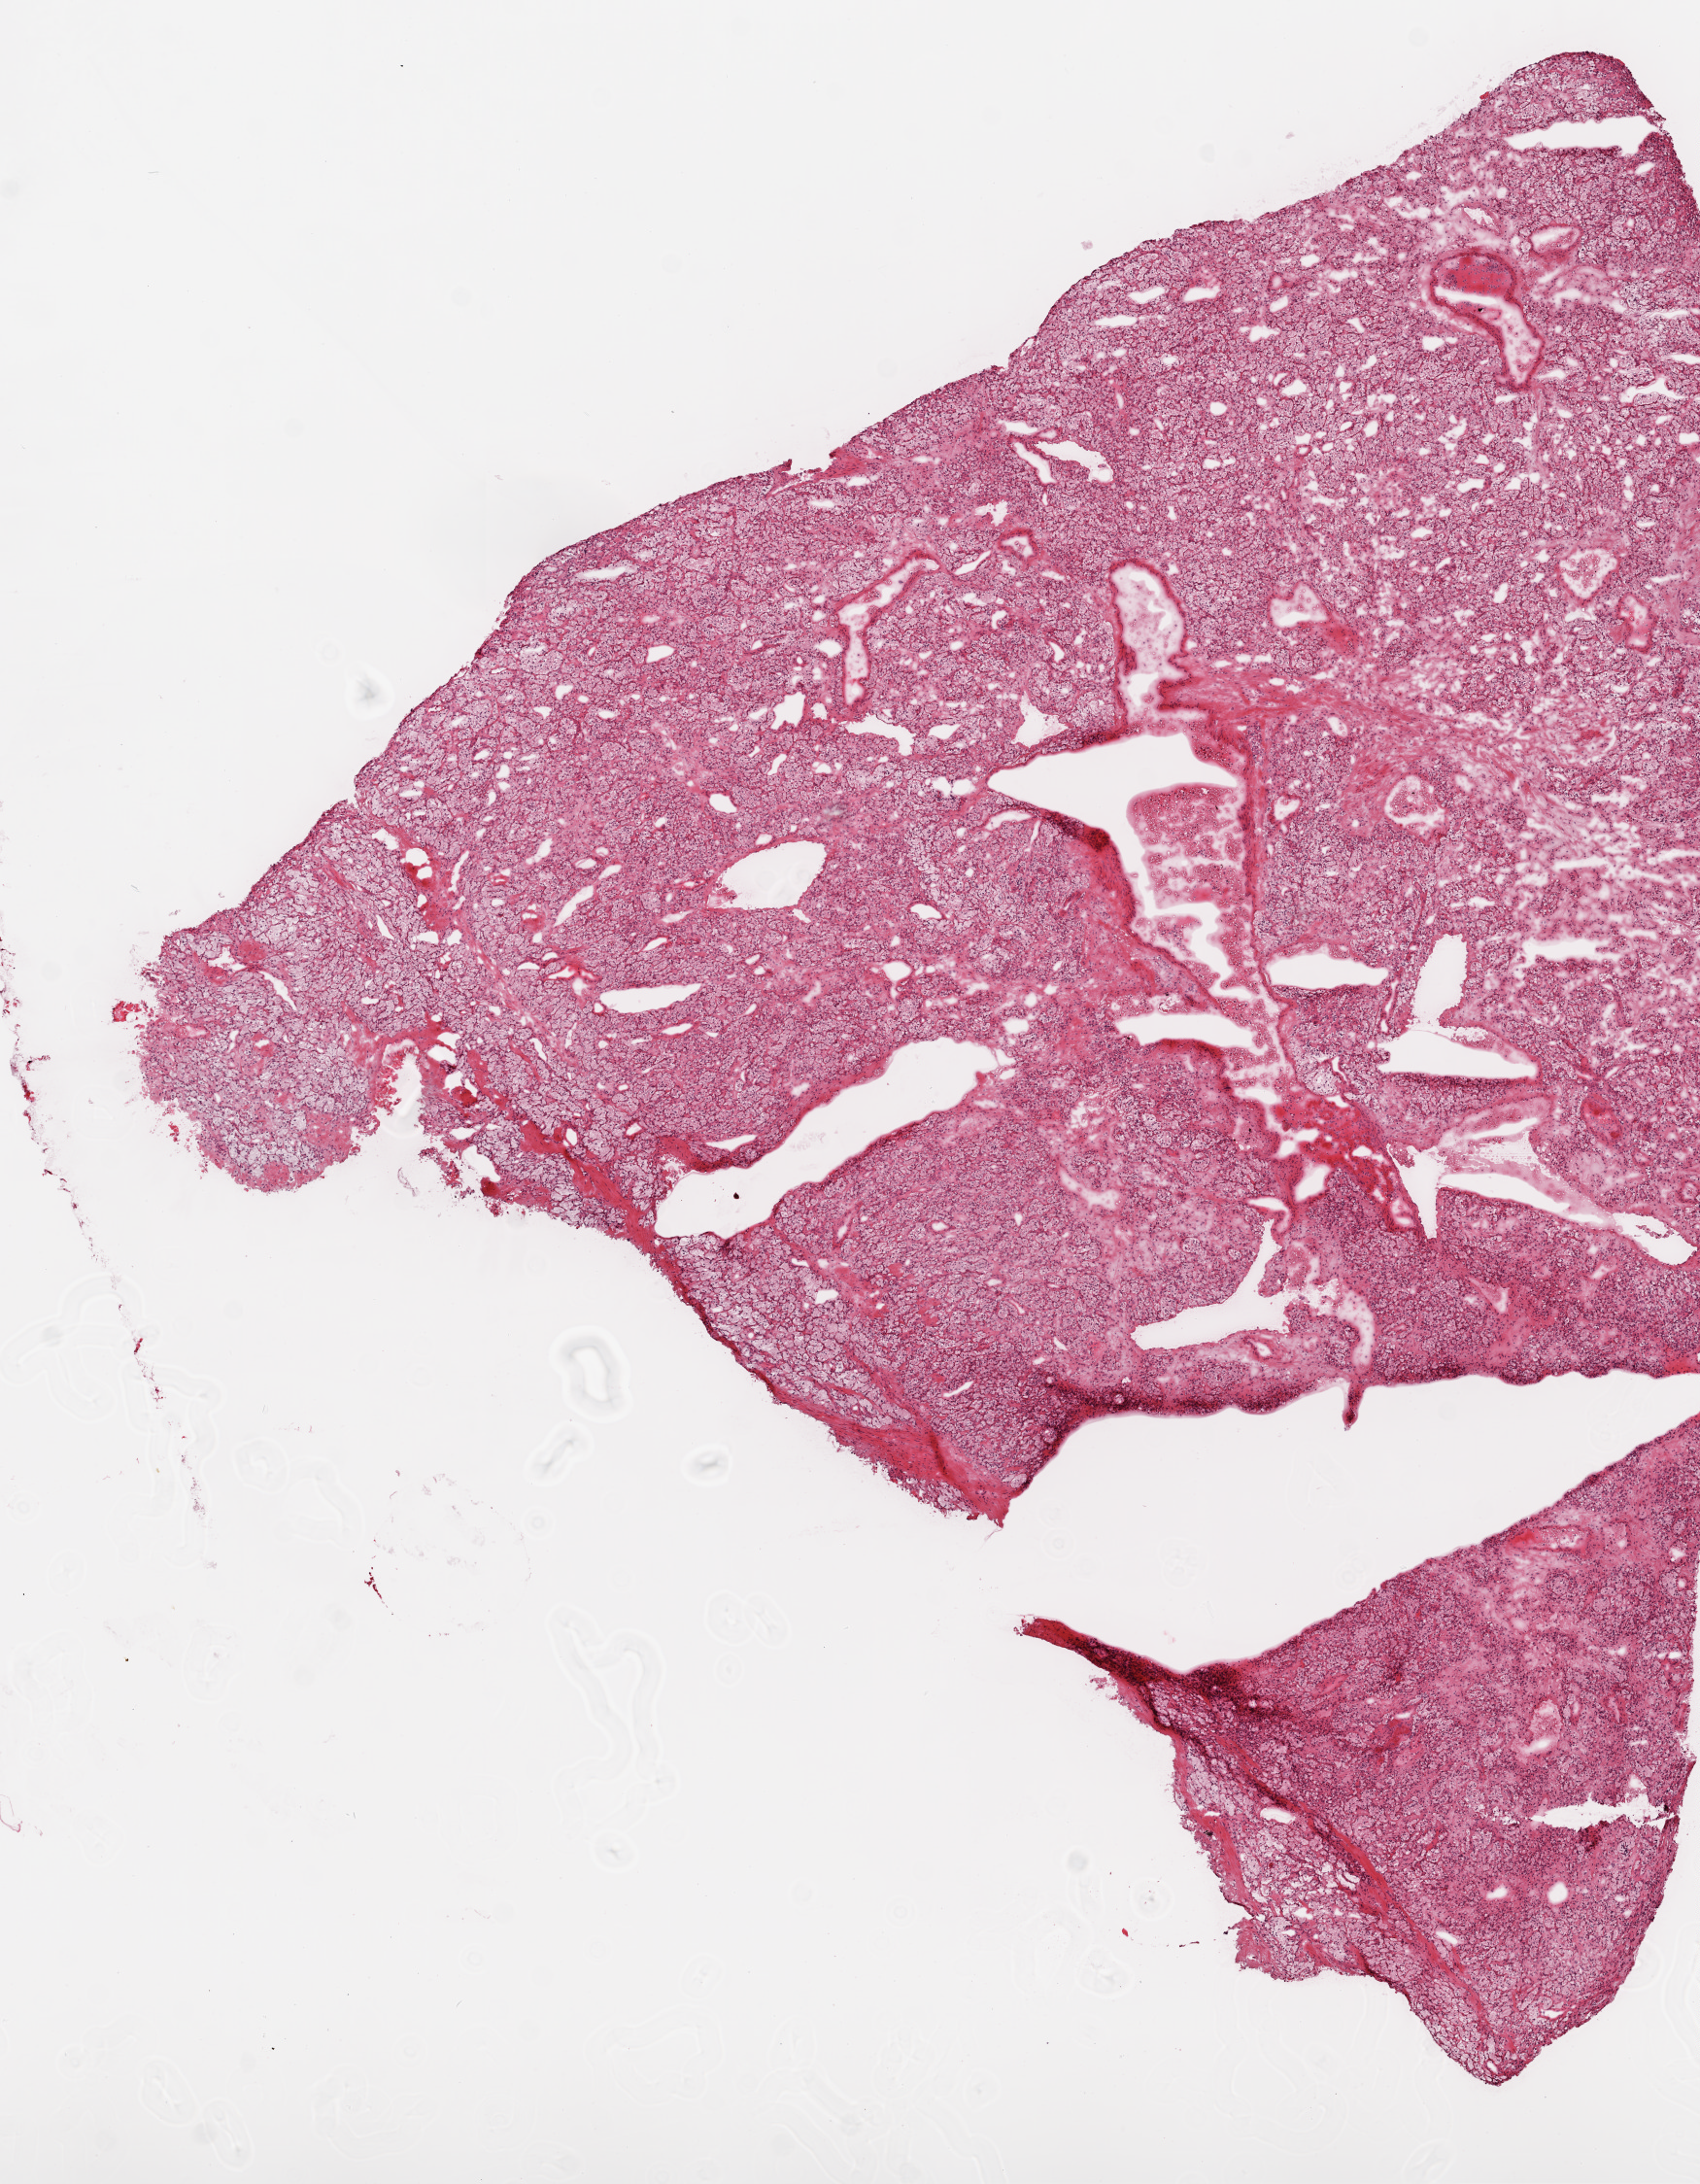
Whole-slide histology image, H&E — whole scanned area (about 7.0 x 9.0 mm, acquisition: 20x scan) shown as a low-resolution overview, frozen section from the top of the tissue portion, kidney, primary tumour sample. Male patient; age at initial diagnosis 48 years. Histologic grade: G2 (moderately differentiated). Pathologist review of this section (percent, as recorded): tumour cells 95%, tumour nuclei 99%, normal cells 0%, stromal cells 5%, necrosis 0%.
Pathologic diagnosis: Clear cell adenocarcinoma, NOS. AJCC pathologic stage: I.